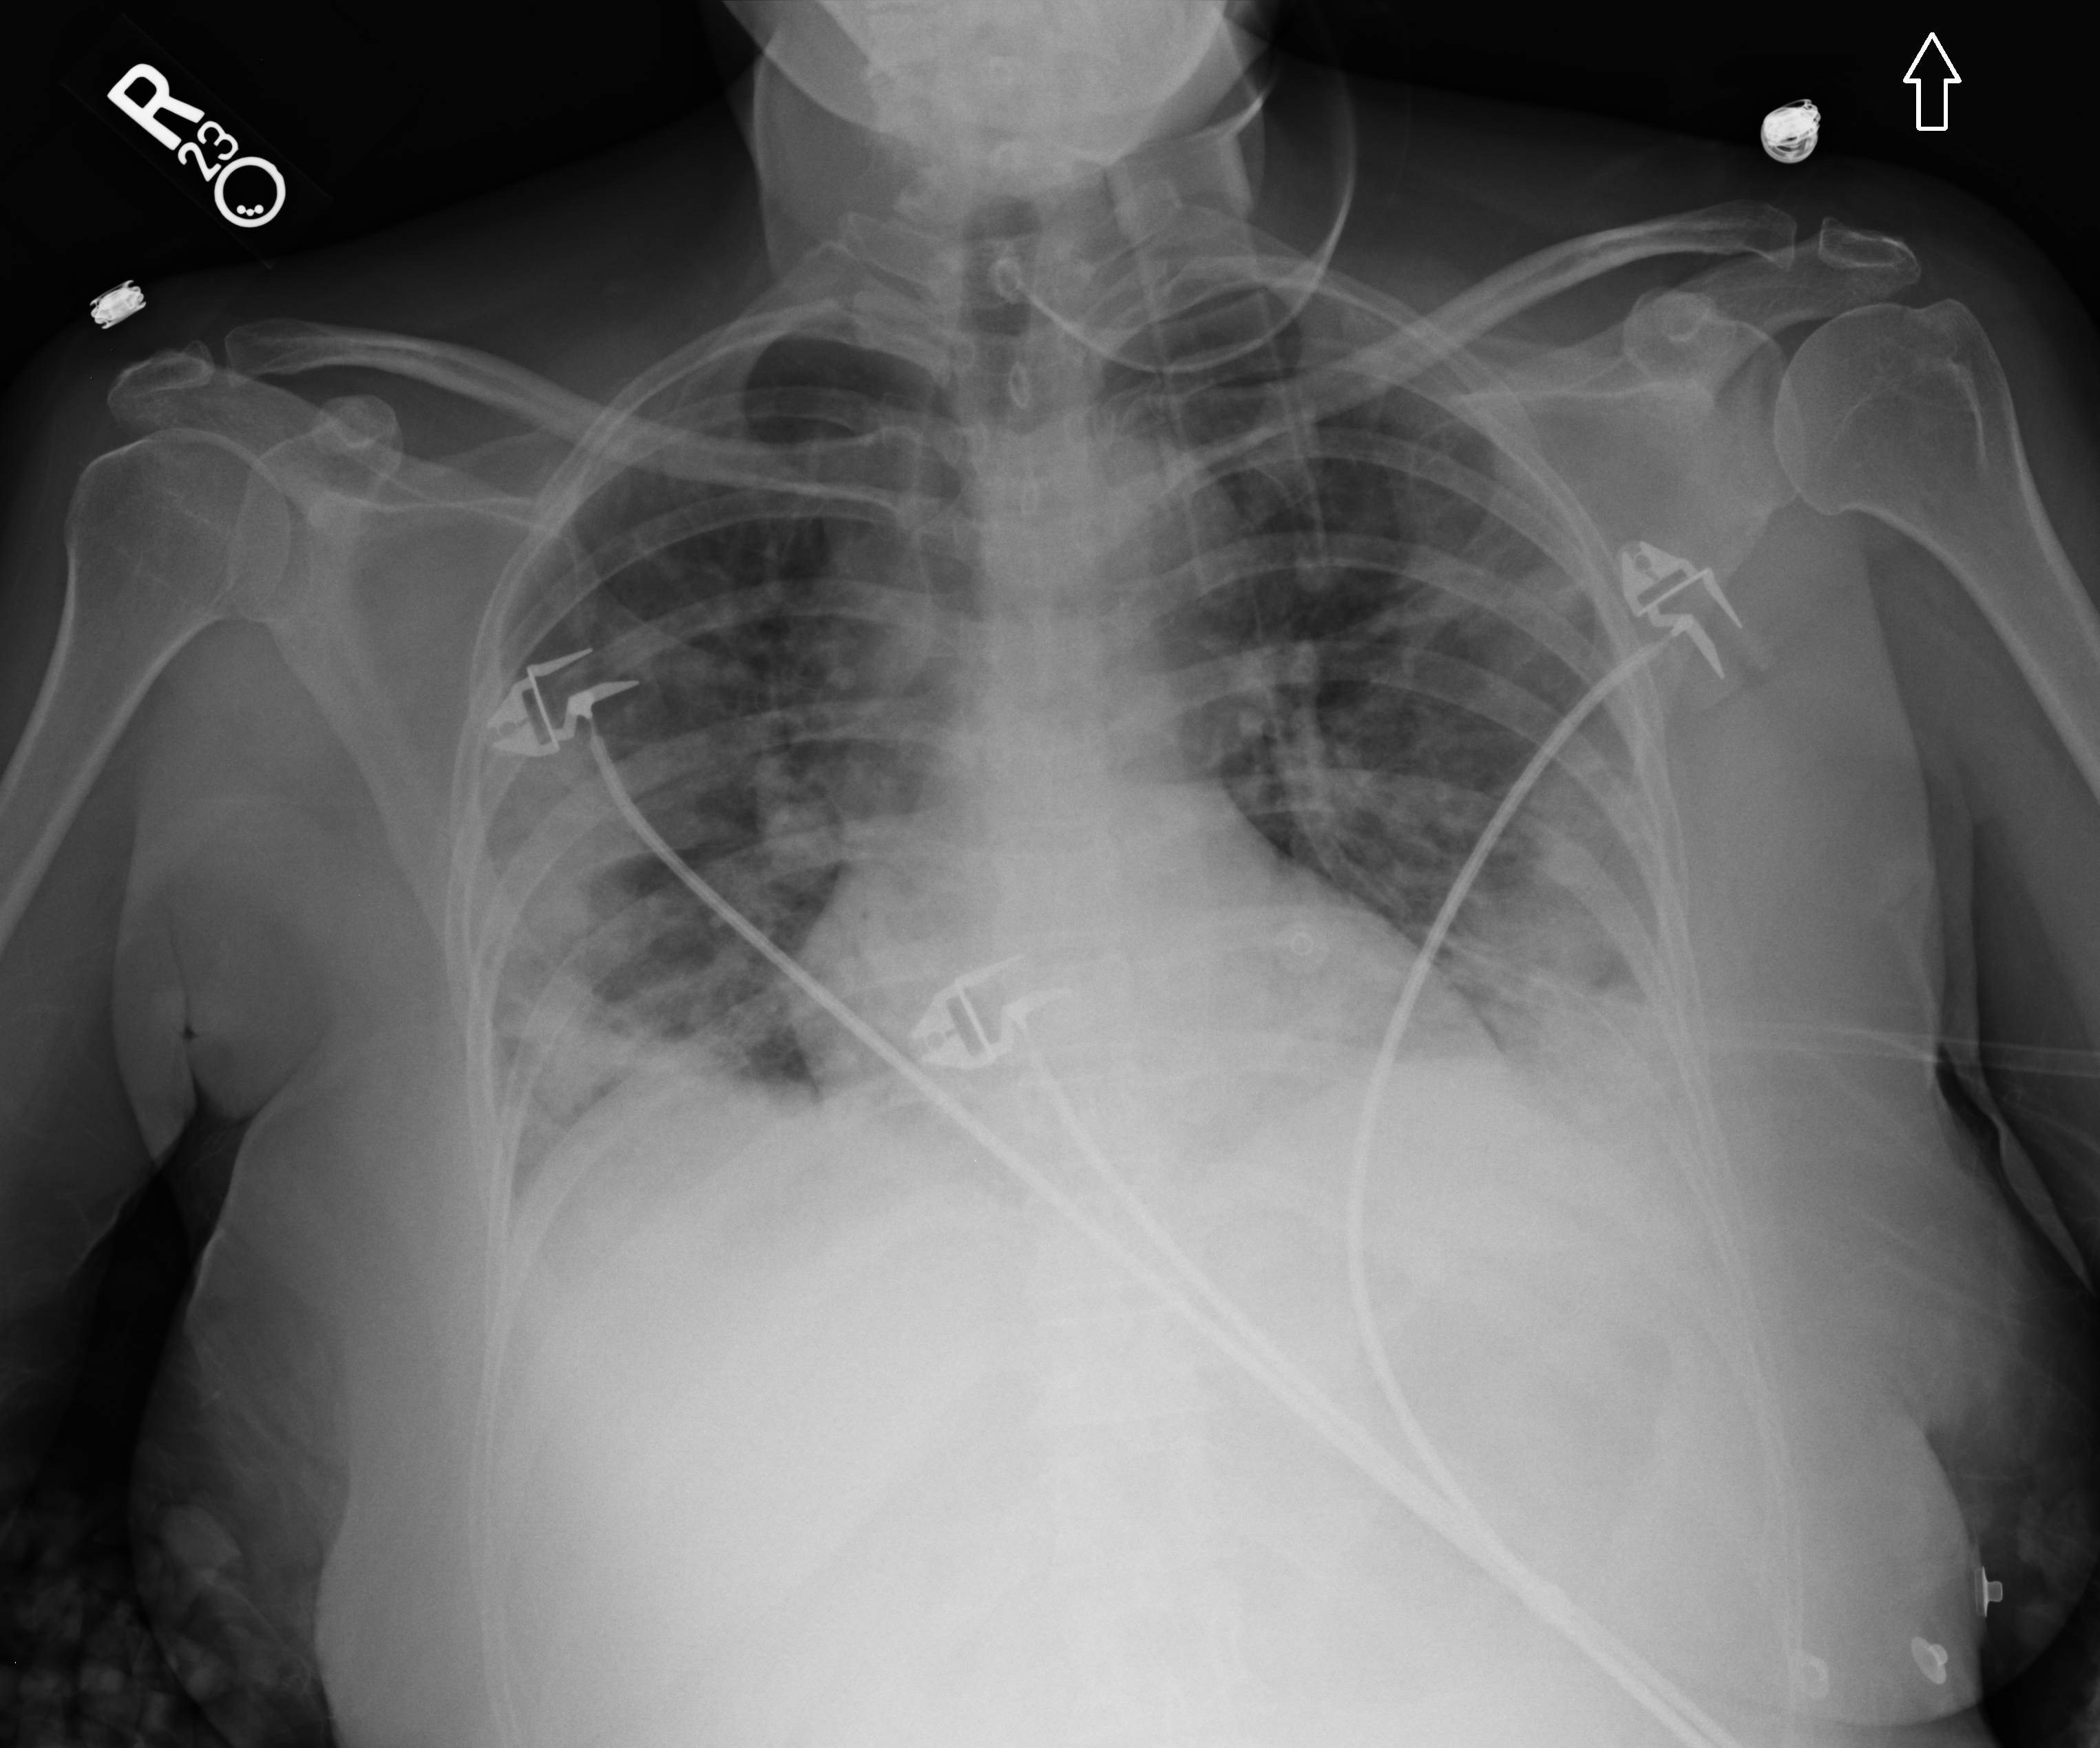
Bedside chest radiograph (computed radiography), anteroposterior (AP) projection. Patient hospitalised with COVID-19; female, aged 18–59 years.
Hospital-stay facts (about this admission, not read from this image; timing relative to this image not recorded):
- length of hospital stay: 16 days